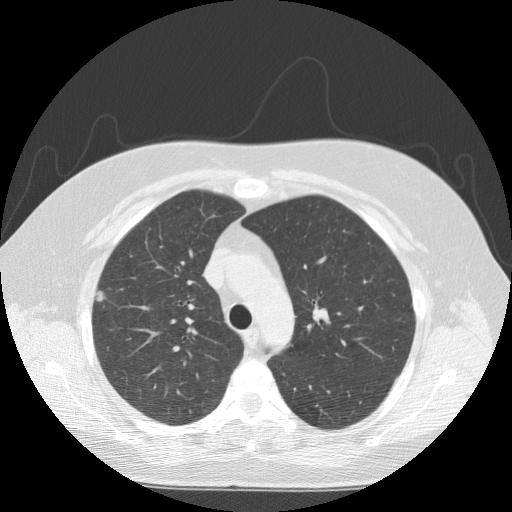
Axial slice from a low-dose chest CT screening exam; baseline annual screen; lung window (W 1500 / L -600 HU); slice 39 of 146 in the series; 512 × 512 image matrix. Female participant, aged 55 years at enrolment. Current smoker at enrolment.
Expert reader's lesion annotation, box from (x=80, y=282) to (x=120, y=319) px. Screening reader's record for this exam (one nodule recorded; not confirmed to be the boxed lesion): non-calcified nodule or mass ≥4 mm, right upper lobe, 8 × 7 mm, spiculated (stellate) margins, soft tissue attenuation. Official screen result: positive, change unspecified: nodule(s) >= 4 mm or enlarging nodule(s), mass(es), or other non-specific abnormalities suspicious for lung cancer. Participant outcome: lung cancer diagnosed 98 days after this screen — squamous cell carcinoma, NOS, right upper lobe, poorly differentiated (G3), stage IA (AJCC 6th edition), 8 mm at pathology.